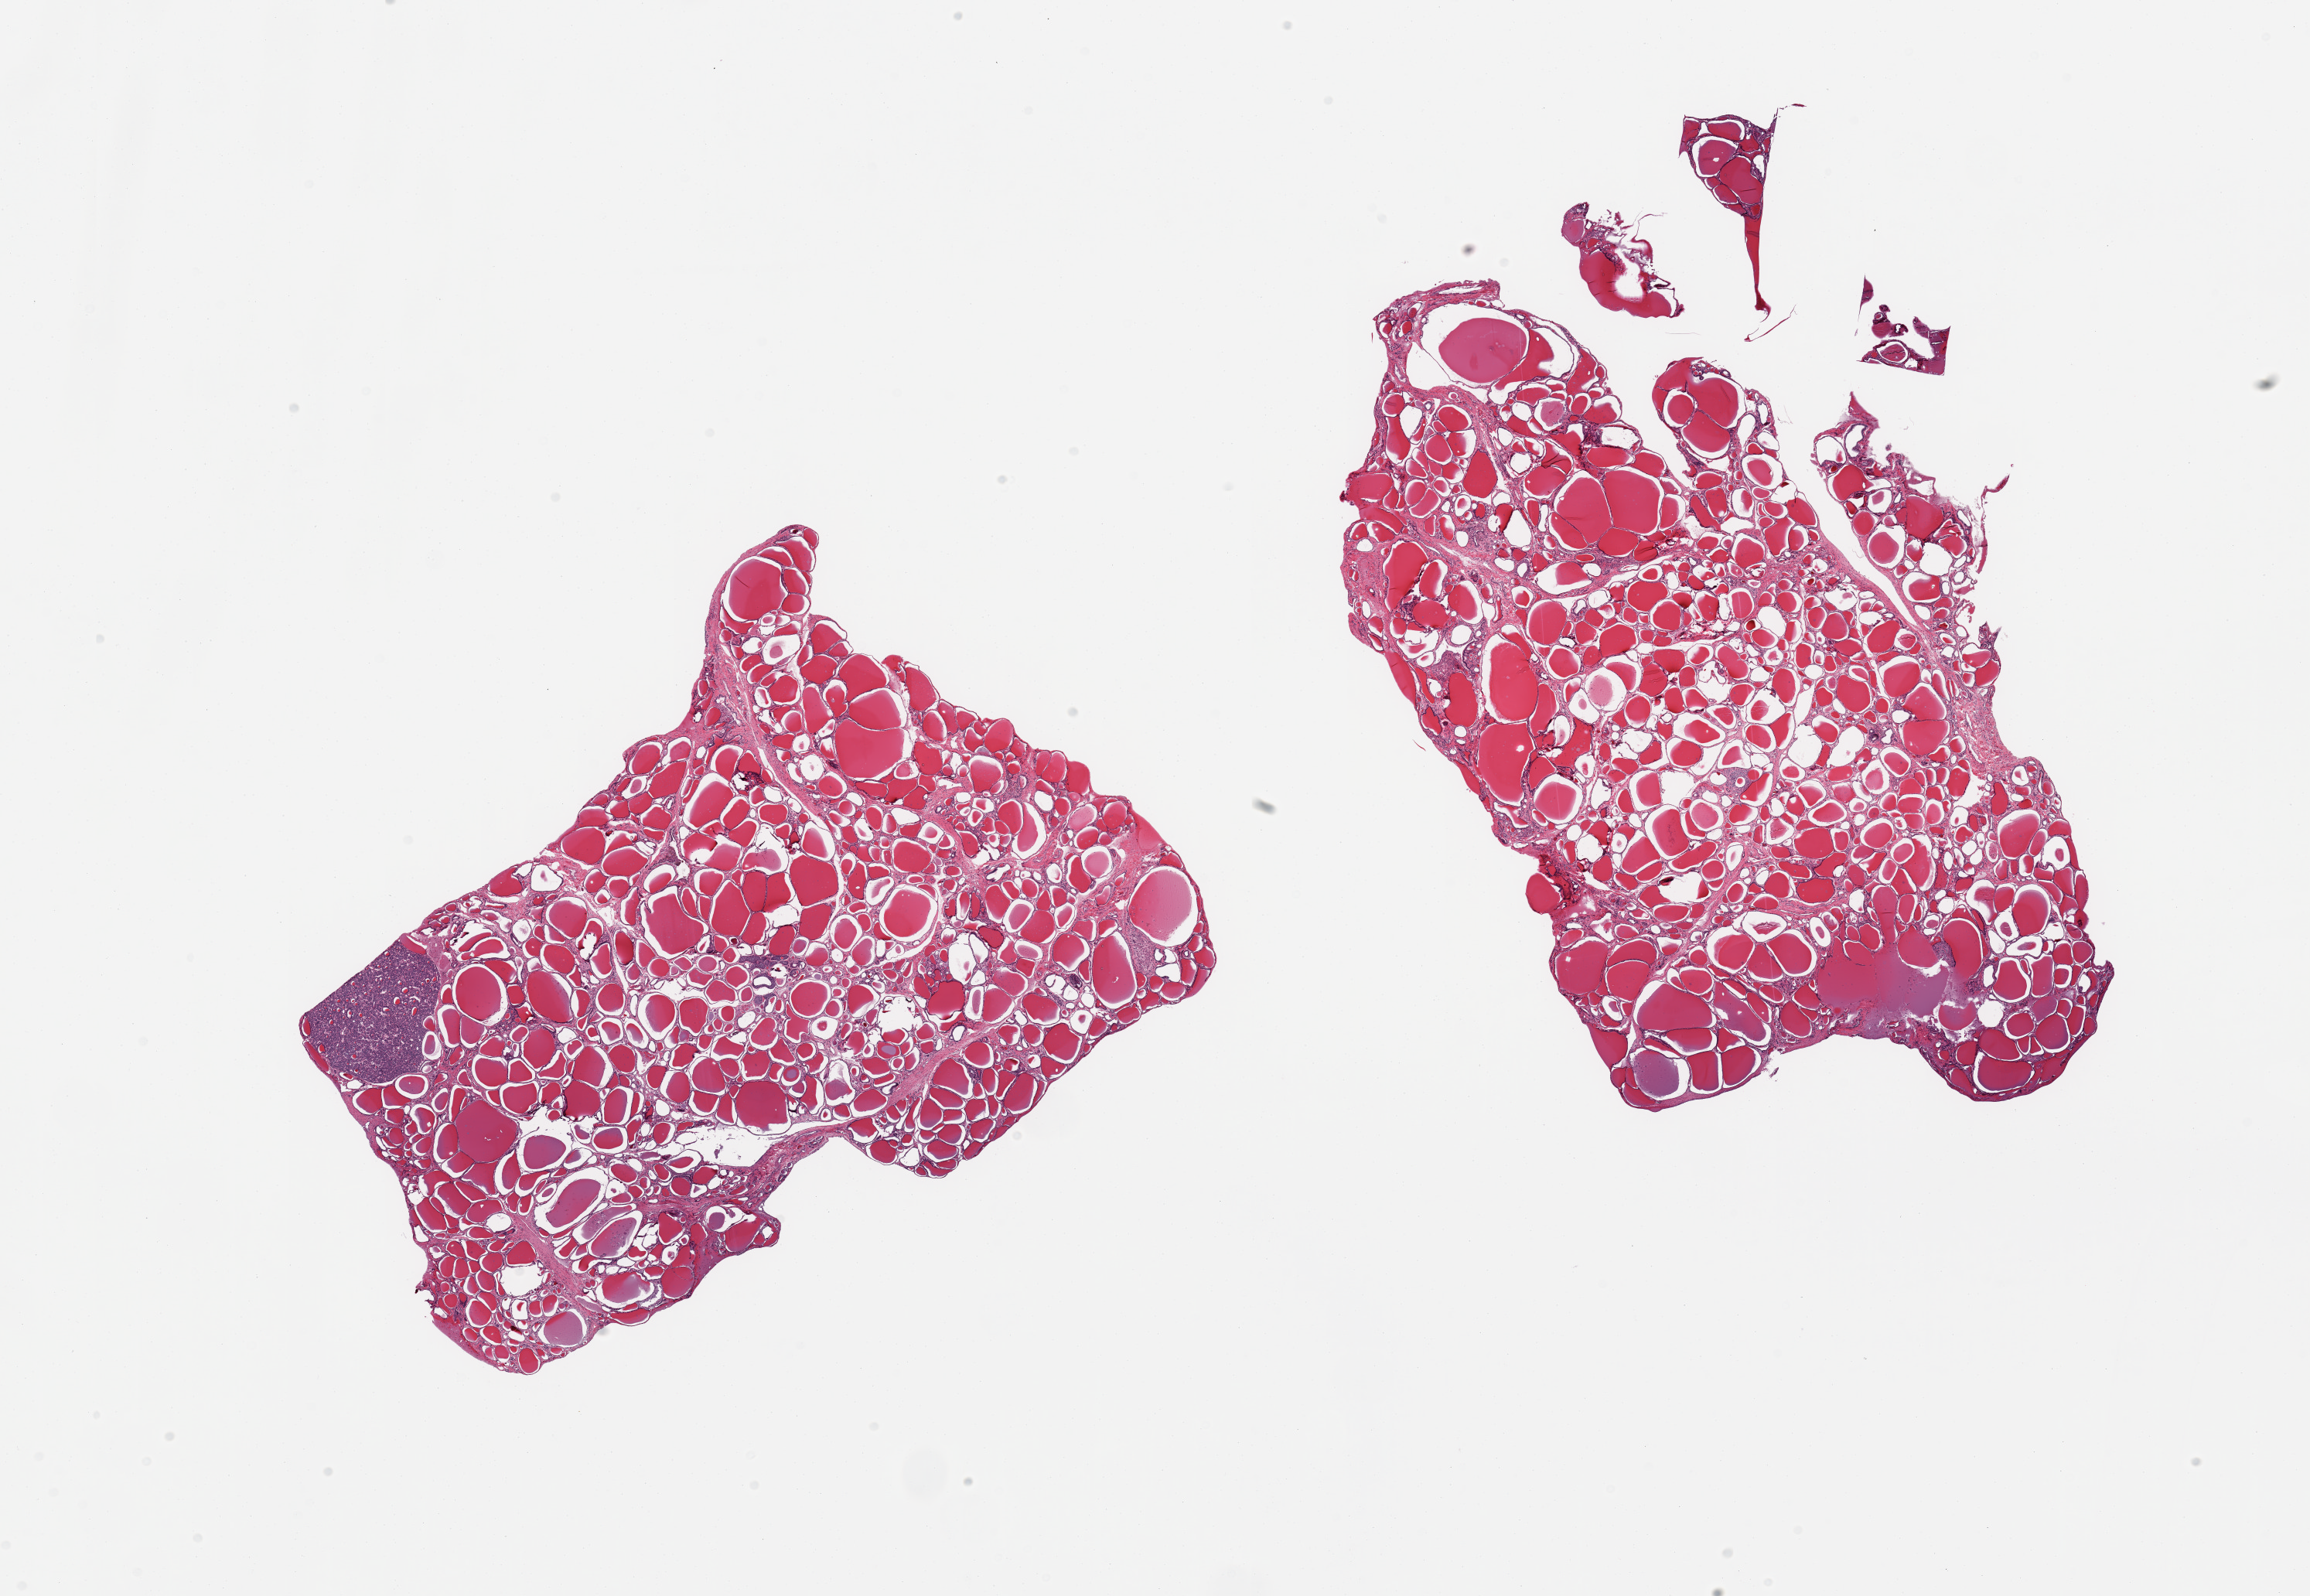
Digitized hematoxylin and eosin (H&E)-stained section, whole scanned area (about 23.6 x 16.3 mm) shown as a low-resolution overview; PAXgene-fixed paraffin-embedded (PFPE) section; sampled site (target tissue): thyroid; tissue donor sample. Donor: male.
- review note (as recorded): 2 pieces, incidental 1.5mm adenoma